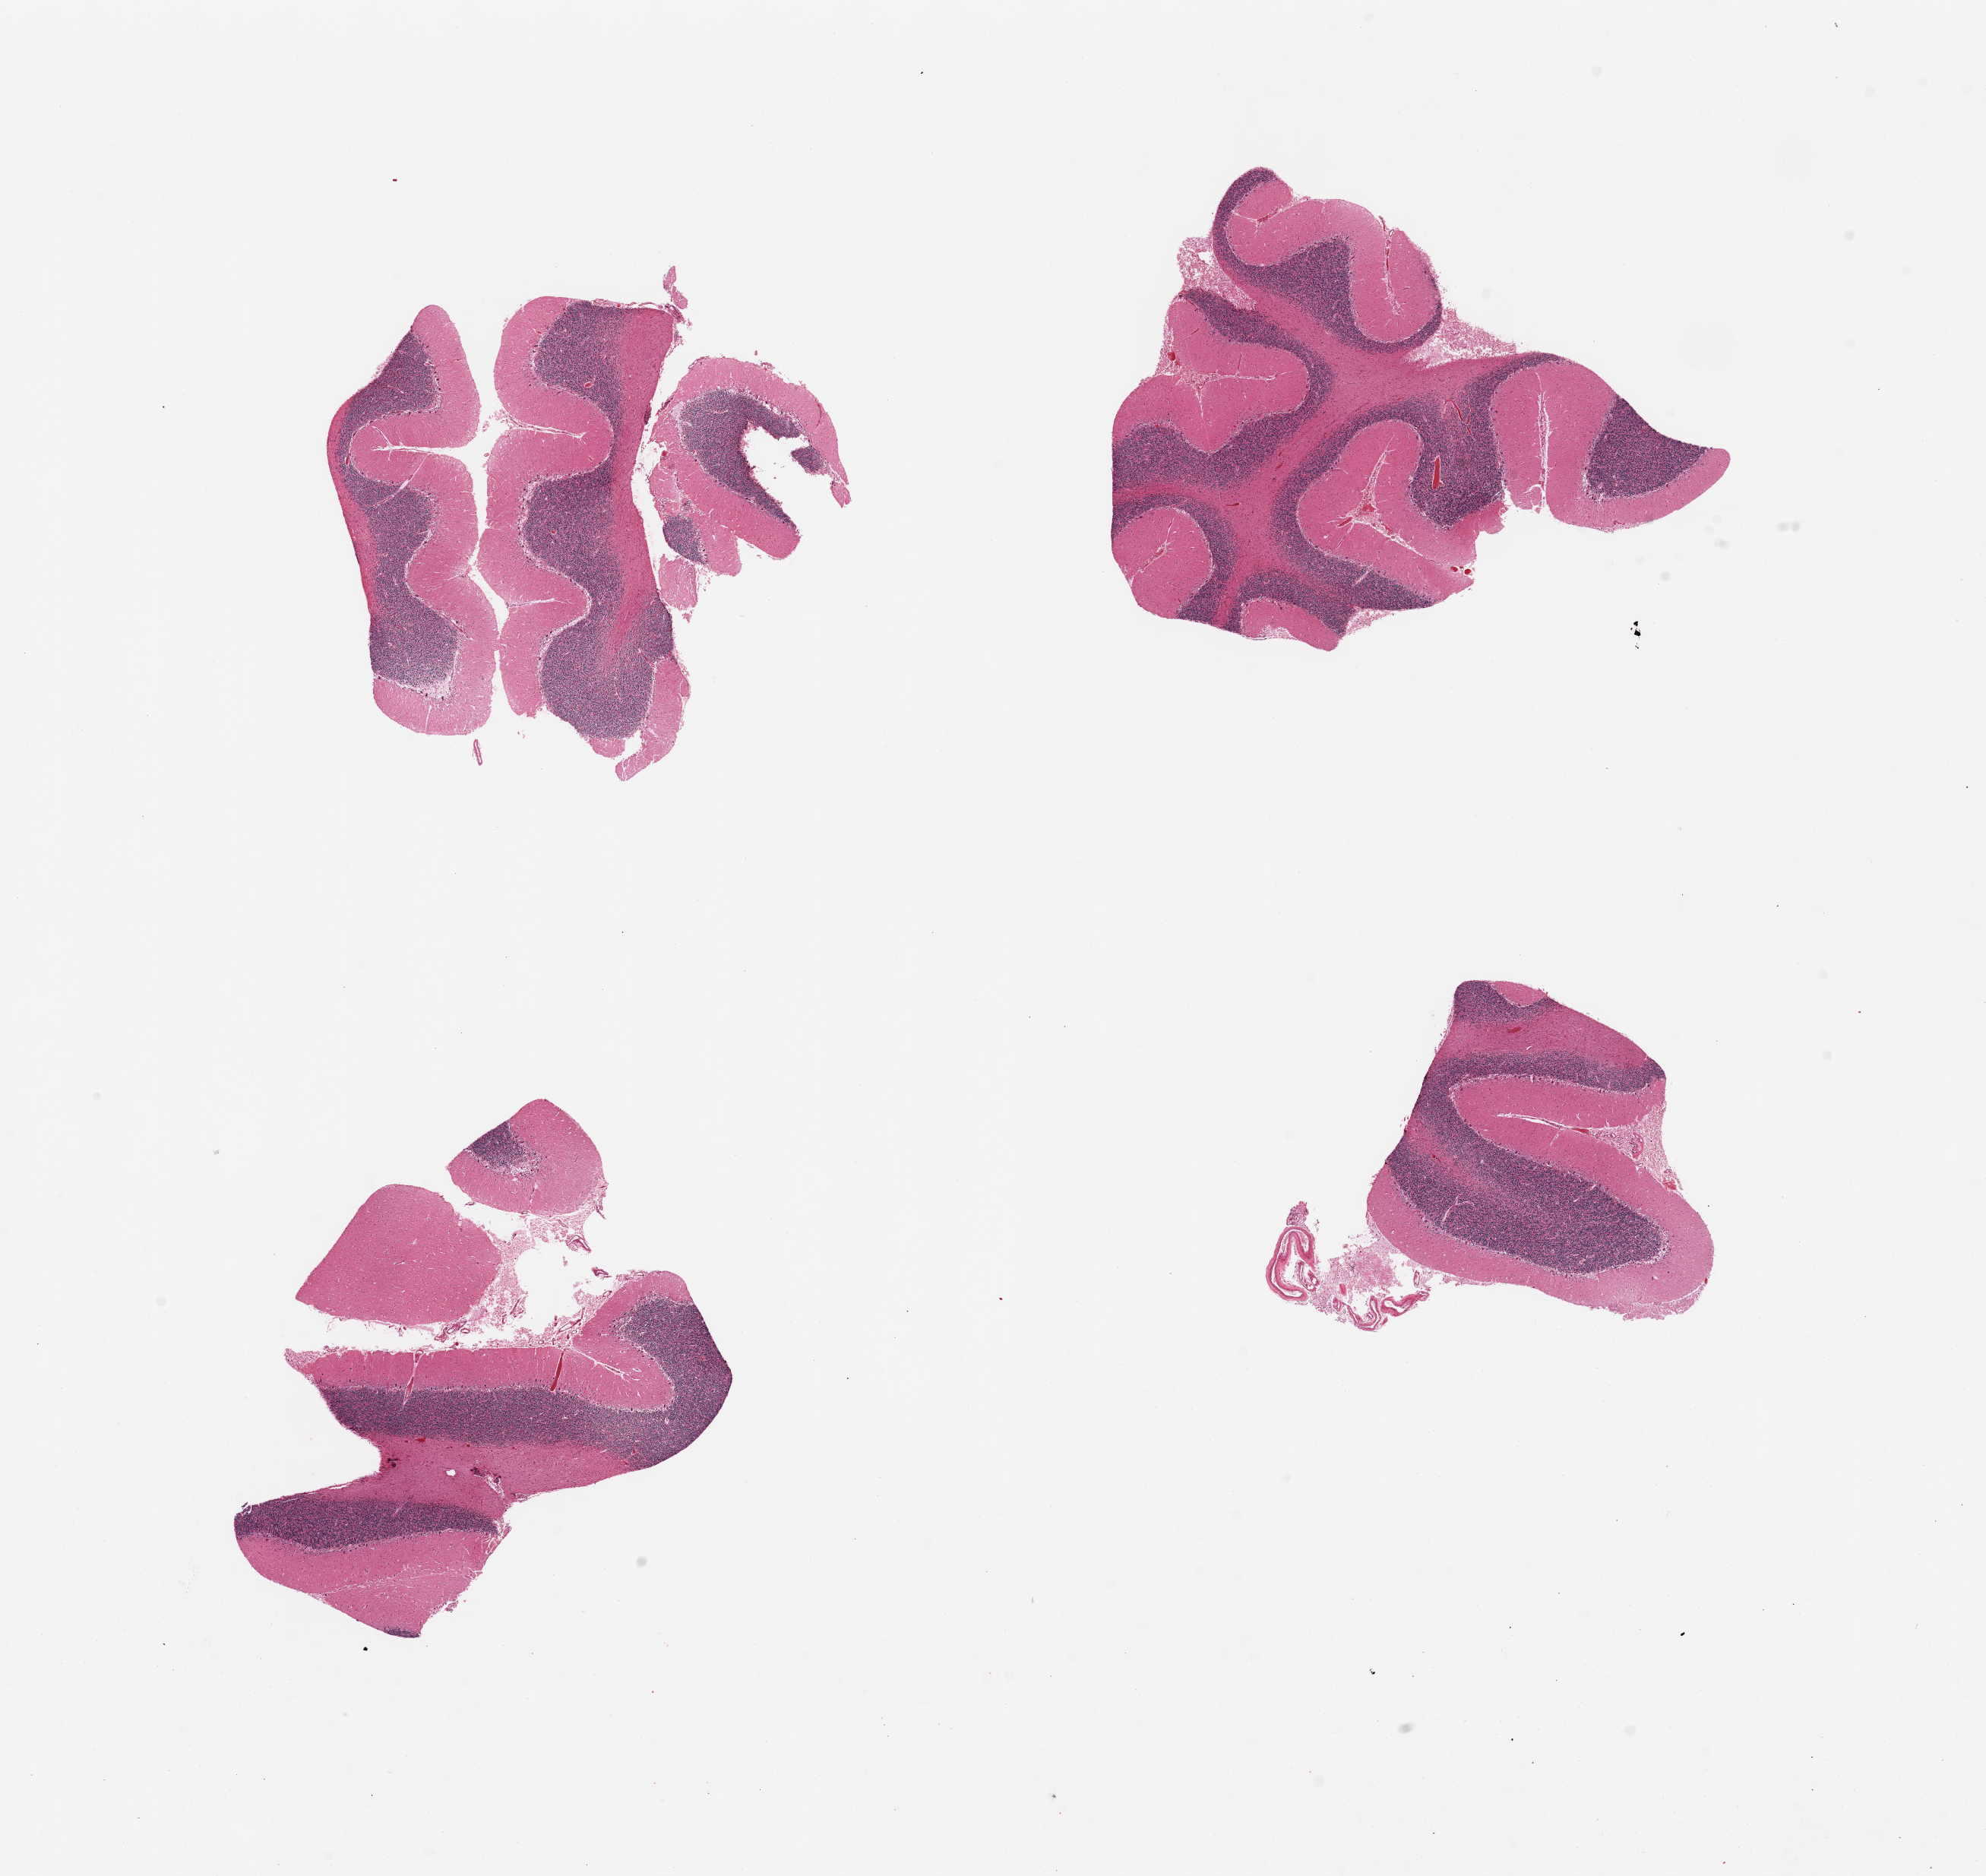
Digitized H&E-stained section, whole scanned area (about 20.7 x 19.5 mm) shown as a low-resolution overview, PAXgene-fixed paraffin-embedded (PFPE) section, sampled site (target tissue): cerebellum, donor tissue sample. Donor: female.
Review note (as recorded): 4 pieces.